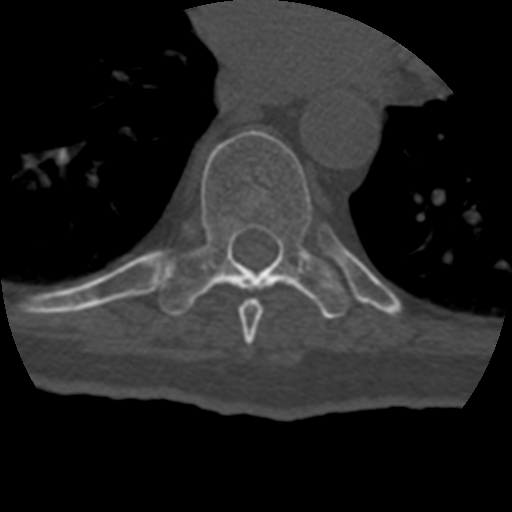
CT including the spine, one axial slice; position 245 of 399 along the scan axis; reconstruction kernel STANDARD; bone window (W 1800 / L 400 HU); 512 × 512 image matrix, field of view 160 × 160 mm. Patient age 69 years. Case-level facts recorded for this patient, not image findings: primary cancer: prostate.
Outlined on this slice (semi-automatic segmentation, software-assisted and operator-edited):
- T8 vertebra: box from (x=239, y=298) to (x=264, y=346) px
- T9 vertebra: (x=156, y=130)–(x=351, y=319)